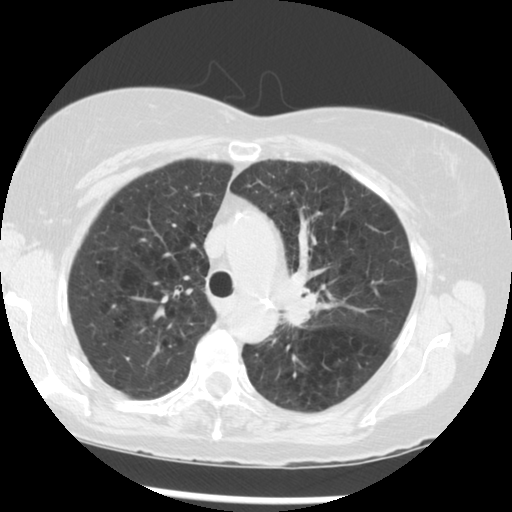
Low-dose screening chest CT, one axial slice. Slice 208 of 283 in the series (ordered by position). Reconstruction kernel STANDARD. Lung window (W 1500 / L -600 HU). 2.5 mm slice thickness. 512 × 512 image matrix, field of view 330 × 330 mm.
Outlined on this slice (outlined manually by an expert reader):
- lesion 1 (tumor, upper lobe of left lung): box from (x=282, y=298) to (x=324, y=326) px